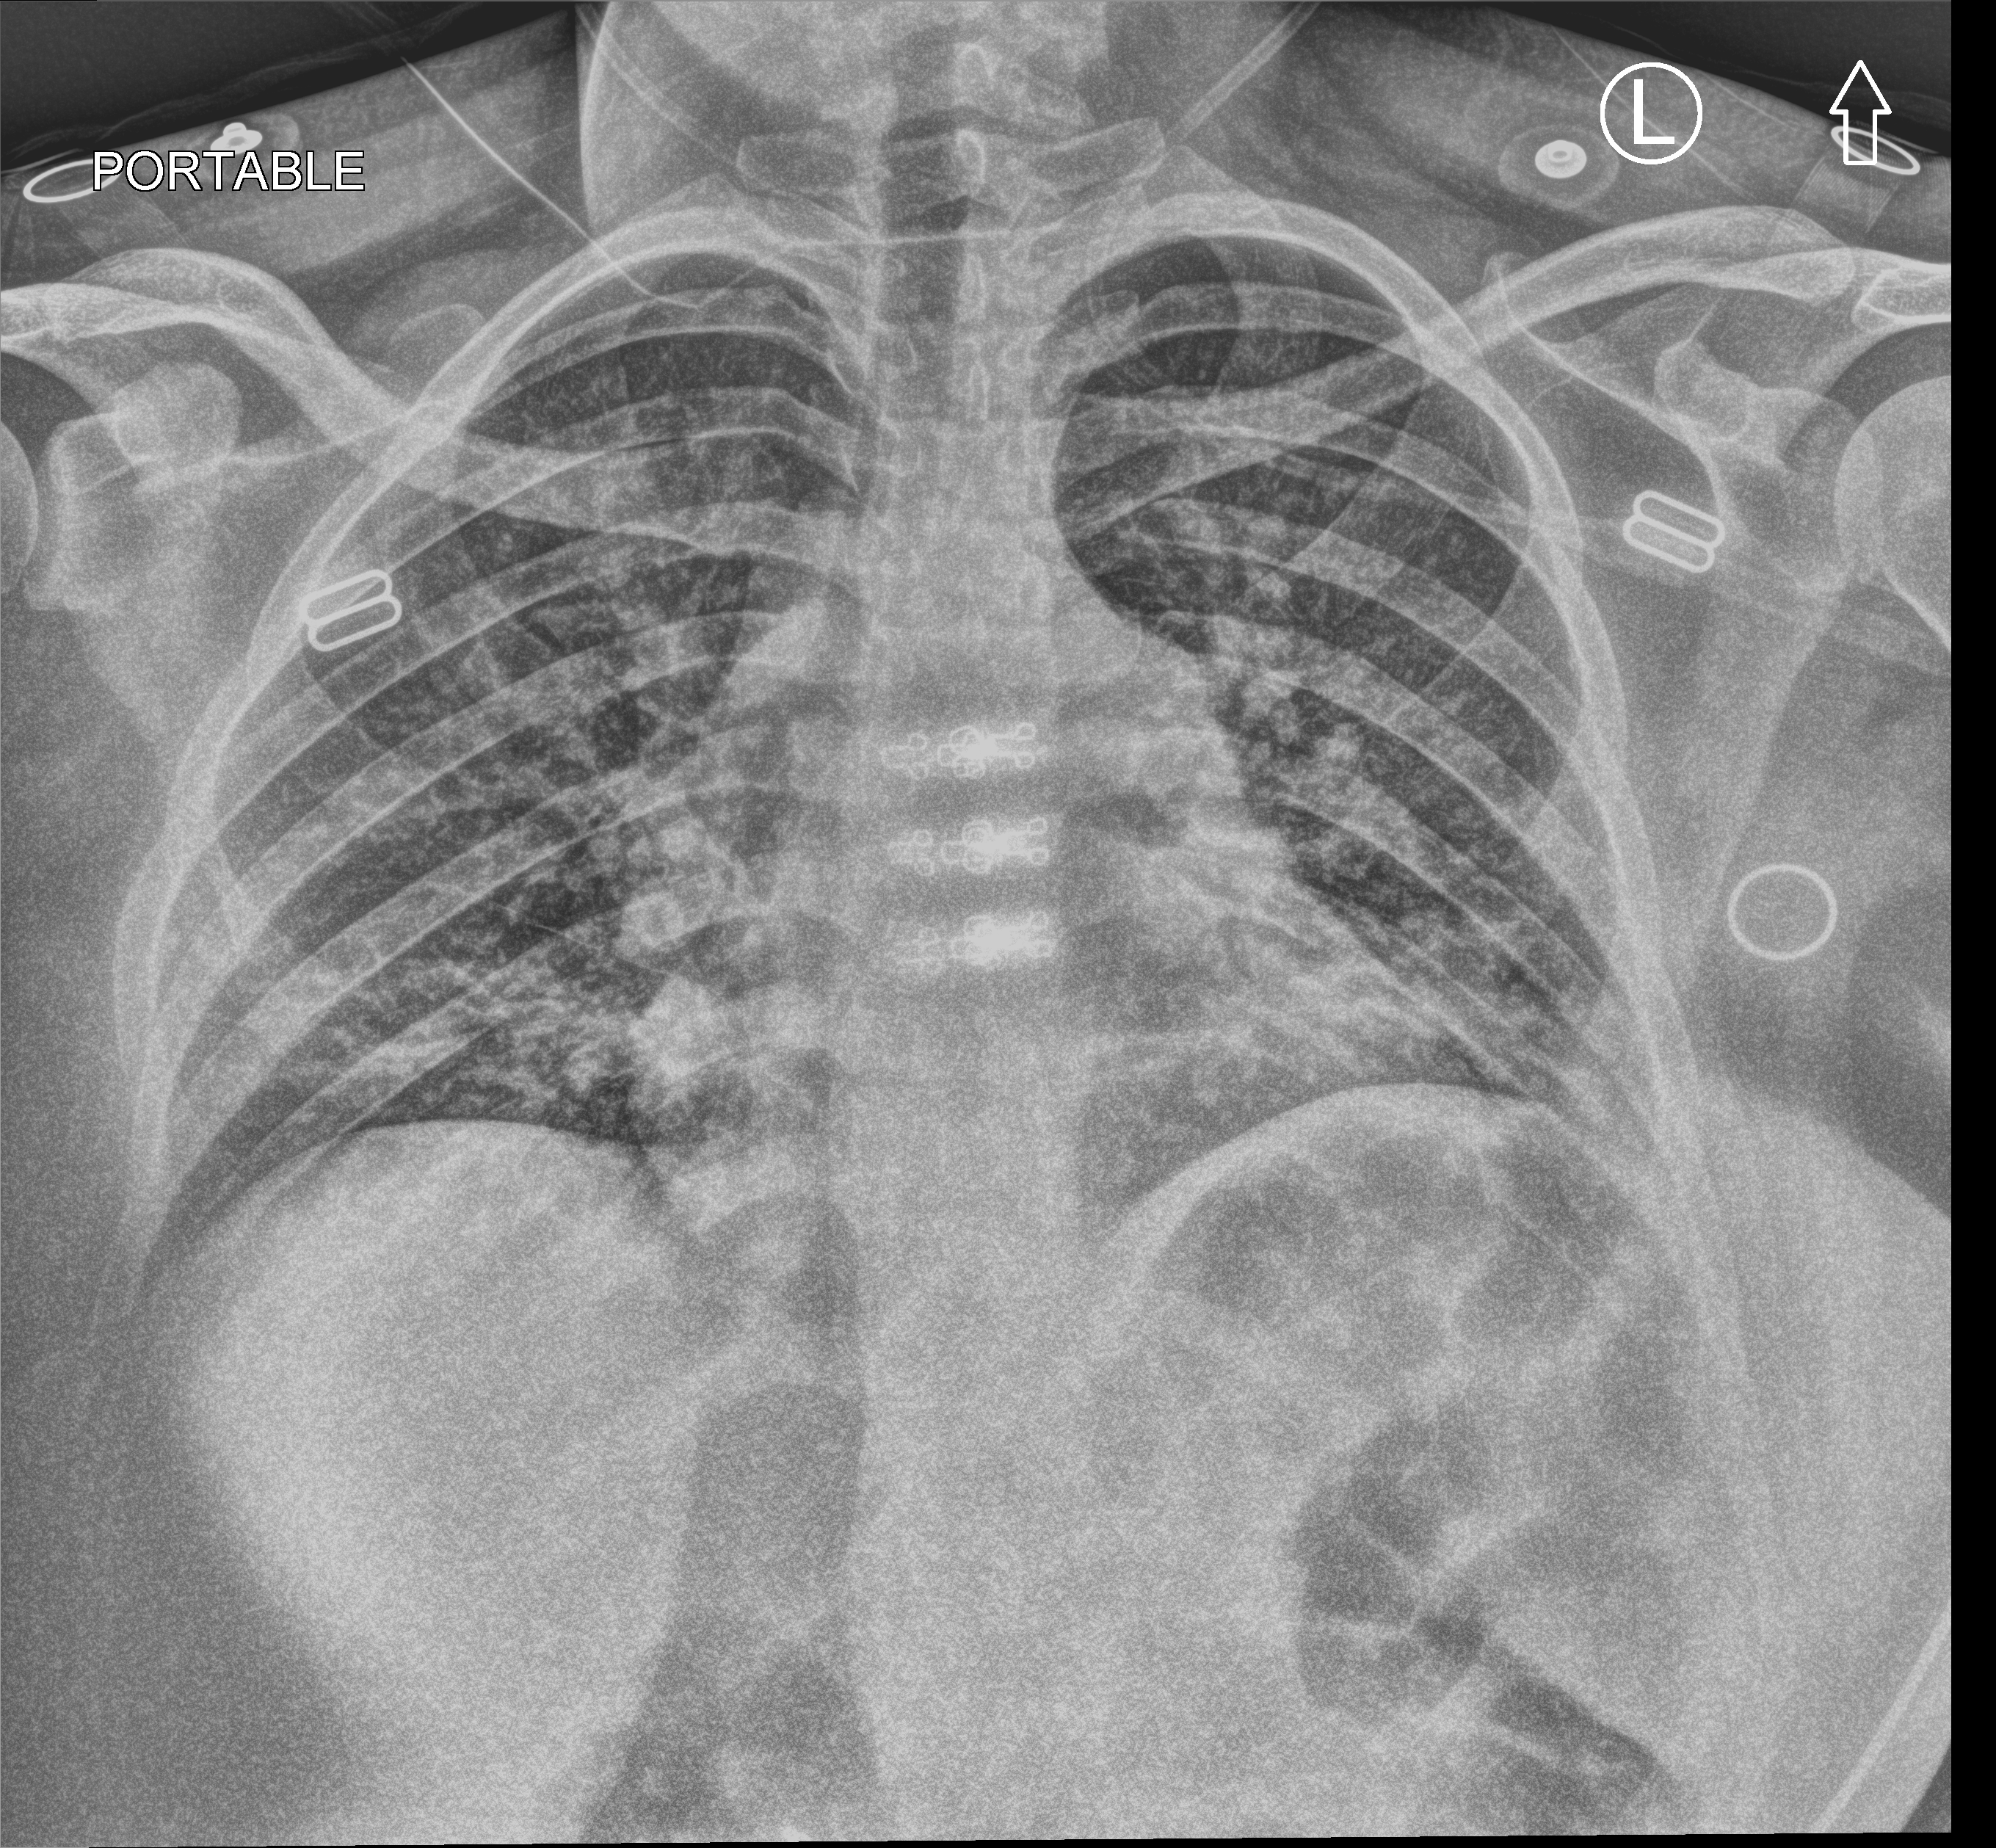
Portable chest radiograph; anteroposterior (AP) projection. Female patient hospitalised with COVID-19, age 18–59 years.
Hospital-stay facts (about this admission, not read from this image; timing relative to this image not recorded): hypertension (admission record): no; mechanically ventilated during this hospital stay: no; admitted to intensive care during this hospital stay: no.